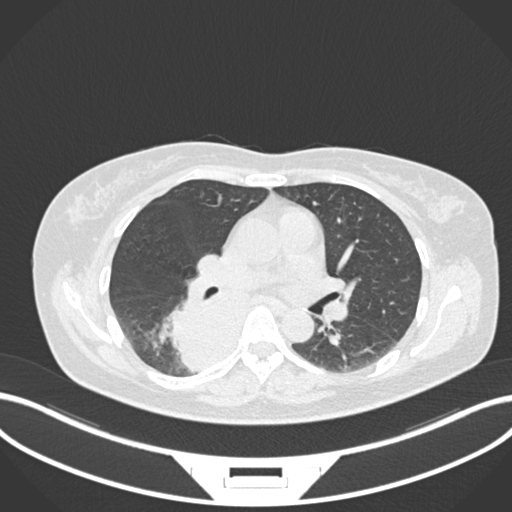
Chest CT, one axial slice. Position 599 of 677 along the scan axis. Reconstruction kernel B30f. 120 kVp. Lung window (W 1500 / L -600 HU). 512 × 512 image matrix, field of view 400 × 400 mm. Patient: female, 54 years. Case-level facts recorded for this patient, not image findings: clinical TNM (as recorded): T4 N0 M0.
Outlined on this slice (bounding box drawn by a radiologist):
- lung tumour (recorded histology: adenocarcinoma): bounding box (x1, y1, x2, y2) in pixels: (167, 282, 254, 379)